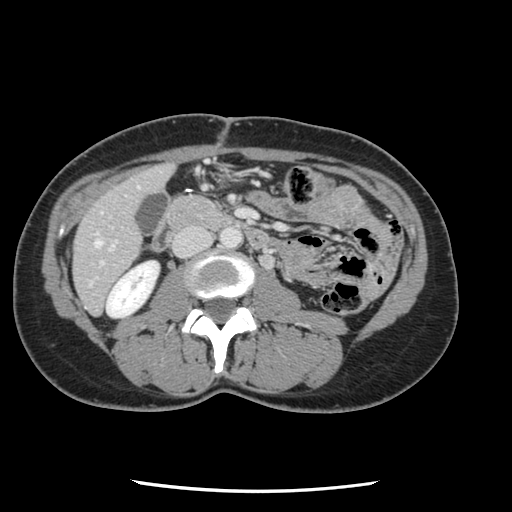
Contrast-enhanced abdominal CT, one axial slice. Position 26 of 134 along the scan axis. Intravenous contrast given. Soft-tissue window (W 400 / L 40 HU). 2.5 mm slice thickness. 512 × 512 image matrix, field of view 330 × 330 mm. Female patient, age 43 years. From the clinical record (not read from this slice): diagnosis: colorectal cancer liver metastases, imaged before liver resection; multiple liver metastases: yes; largest metastasis: 3.4 cm; chemotherapy before resection: no.
Annotated regions visible in this slice (manually delineated by an expert):
- hepatic veins: bounding box [x1, y1, x2, y2] px = [95, 240, 101, 246]
- liver: [75, 166, 173, 313]
- planned liver remnant (the part of the liver to remain after resection): [75, 166, 172, 313]